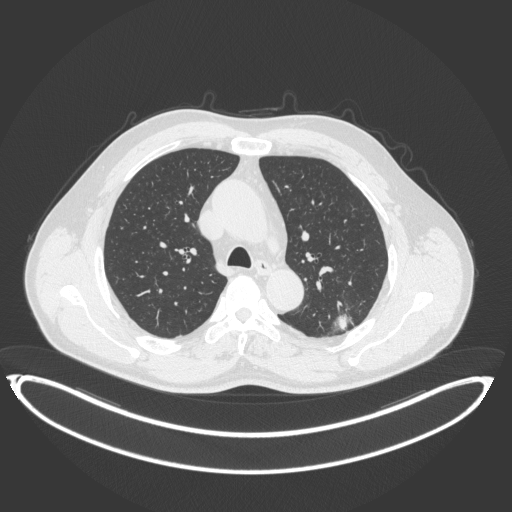
Chest CT, one axial slice. Position 247 of 399 along the scan axis. 120 kVp. Lung window (W 1500 / L -600 HU). 512 × 512 image matrix, field of view 469 × 469 mm. Male patient, age 58 years. From the clinical record (not read from this slice): clinical TNM (as recorded): T1c N0 M0; histopathological grade: G1-2.
Annotated regions visible in this slice (rectangle marked by the reading radiologist):
- lung tumour (recorded histology: adenocarcinoma): bounding box (x1, y1, x2, y2) in pixels: (325, 307, 357, 338)